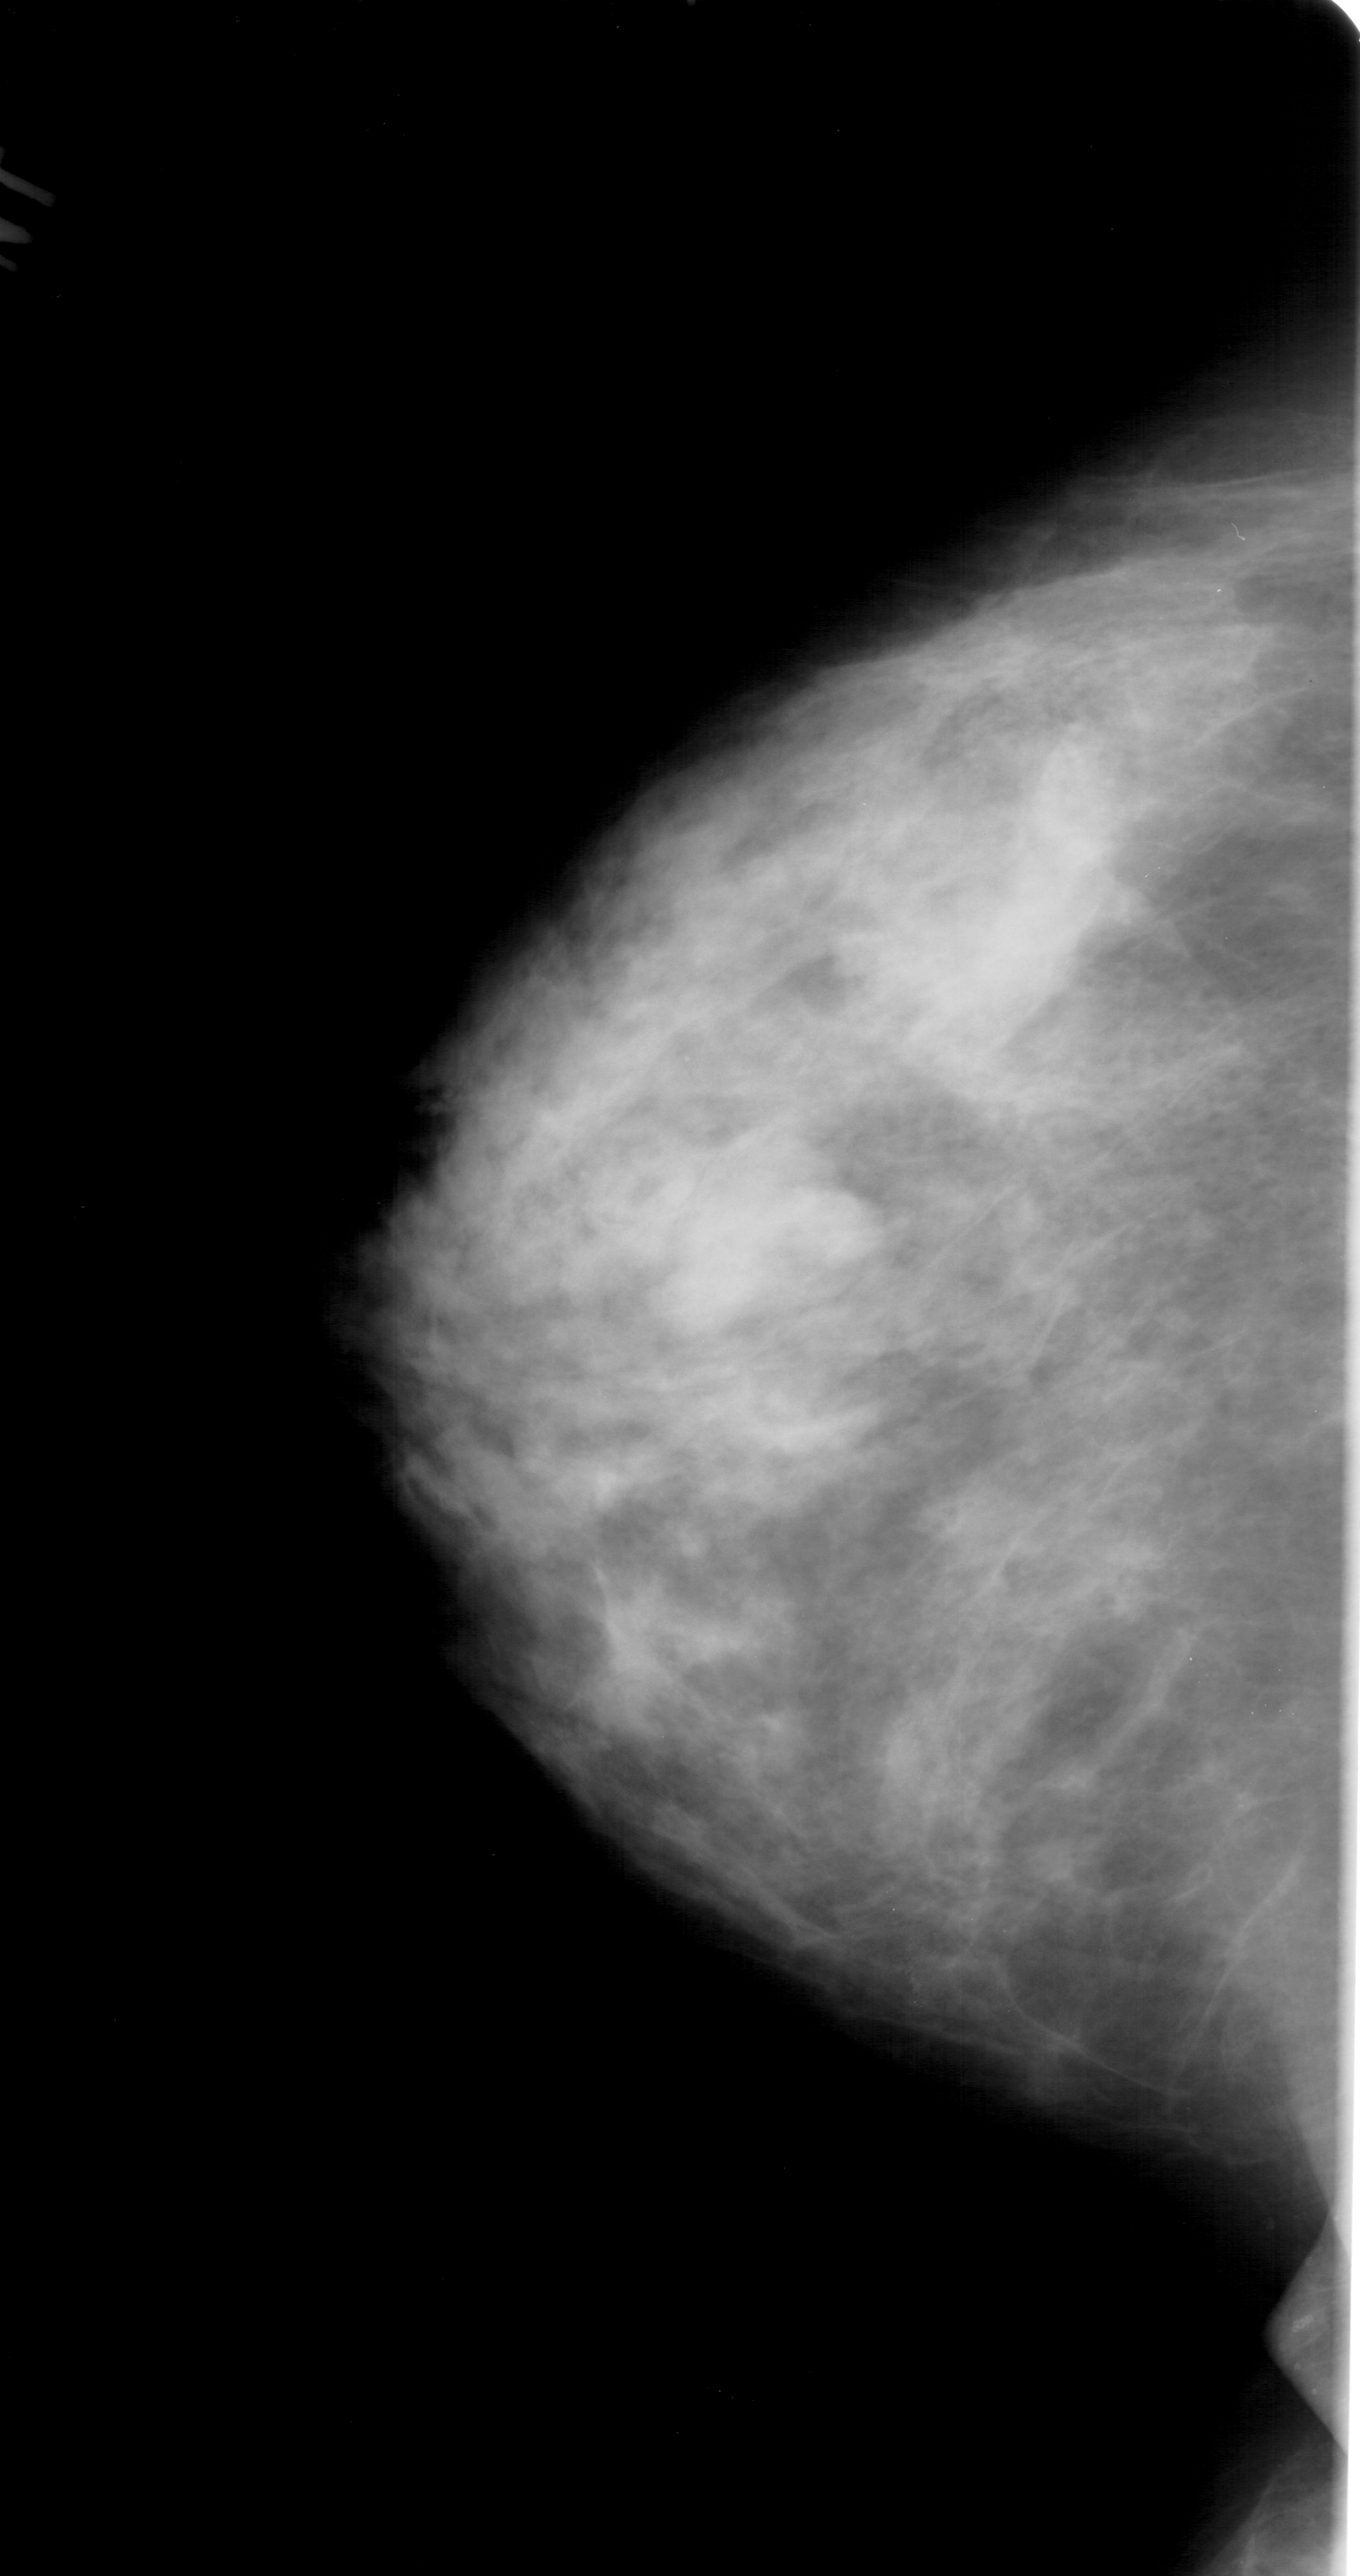
Digitized screen-film mammogram, left breast, CC view, BI-RADS breast density category 3 (scale 1–4).
- Finding: mass, shape lobulated, margins obscured; BI-RADS assessment category 4; pathology result (as recorded, not read from the image): benign.